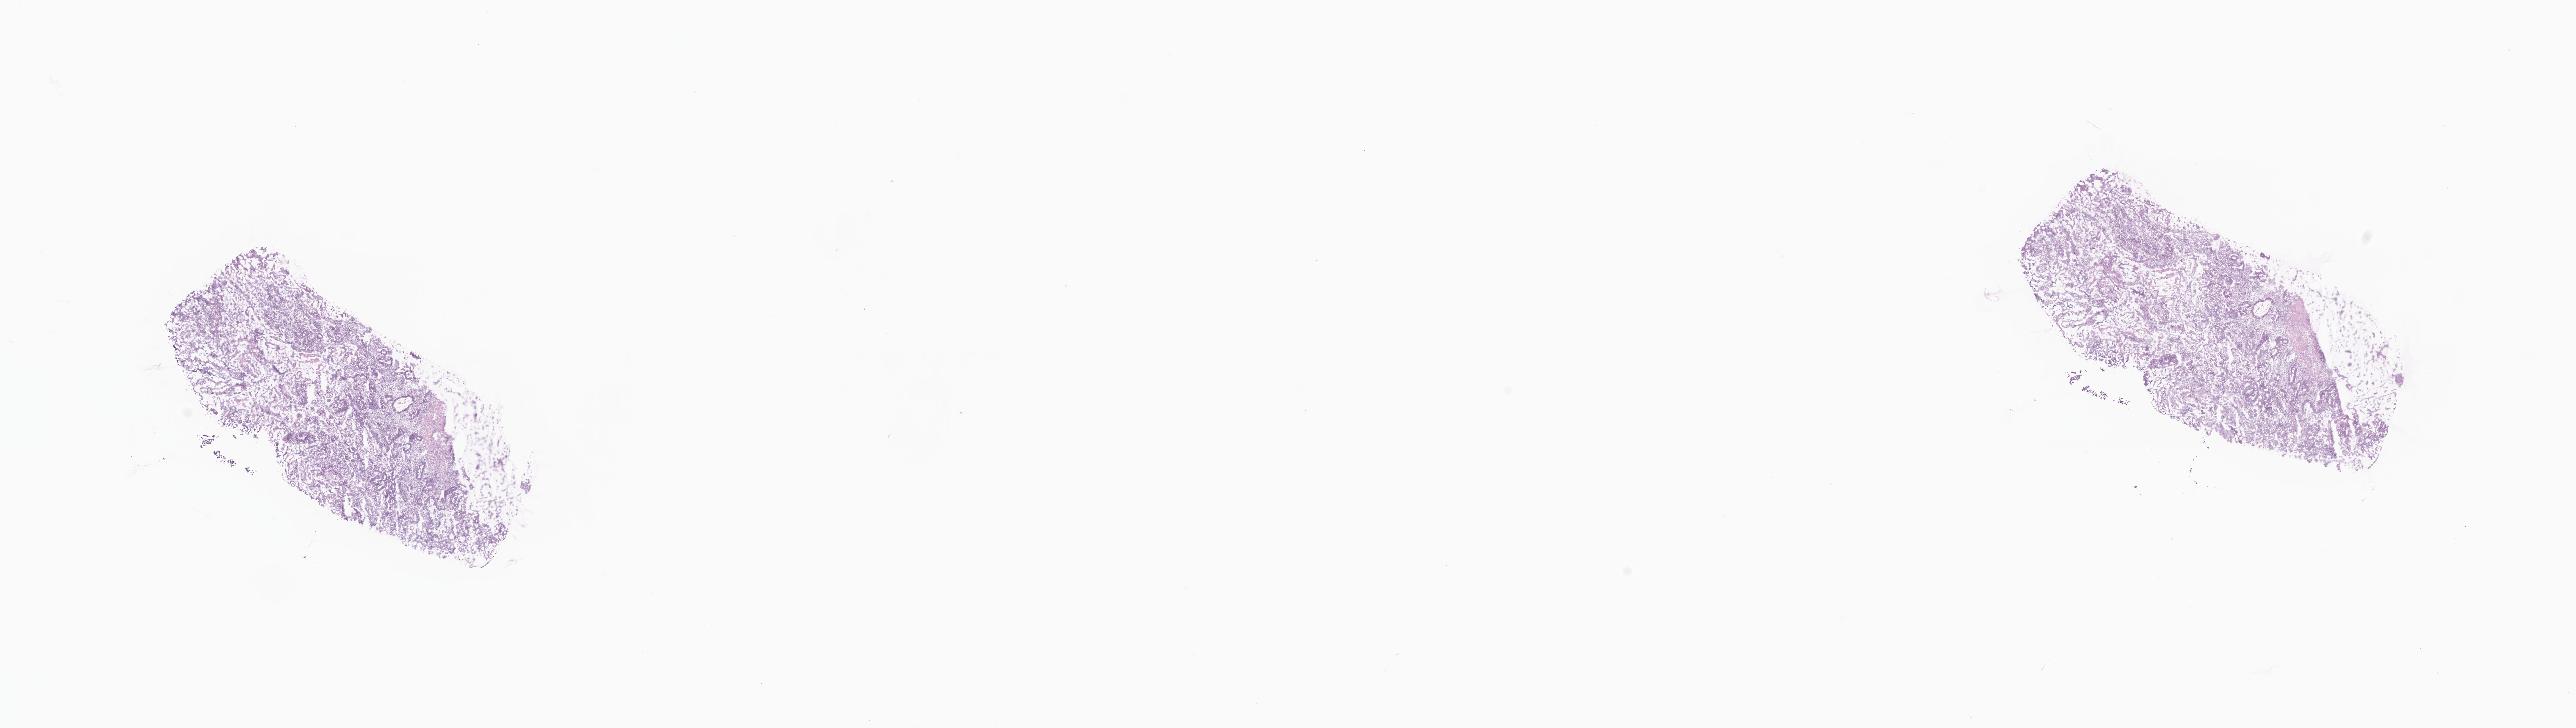
Whole-slide image, H&E stain — a low-resolution overview of the entire scanned area, about 28.7 x 8.1 mm. Frozen section (tissue freezing medium). Primary tumor. Site: rectosigmoid junction. Male, age 63 years at initial diagnosis. Composition of this section per pathologist review: tumor cells 32%, tumor nuclei 38%, stromal cells 64%, necrosis 4%, normal cells 0%. Infiltration values recorded for this section: lymphocyte infiltration 52%, monocyte infiltration 2%, neutrophil infiltration 0%.
• diagnosis: Adenocarcinoma, NOS